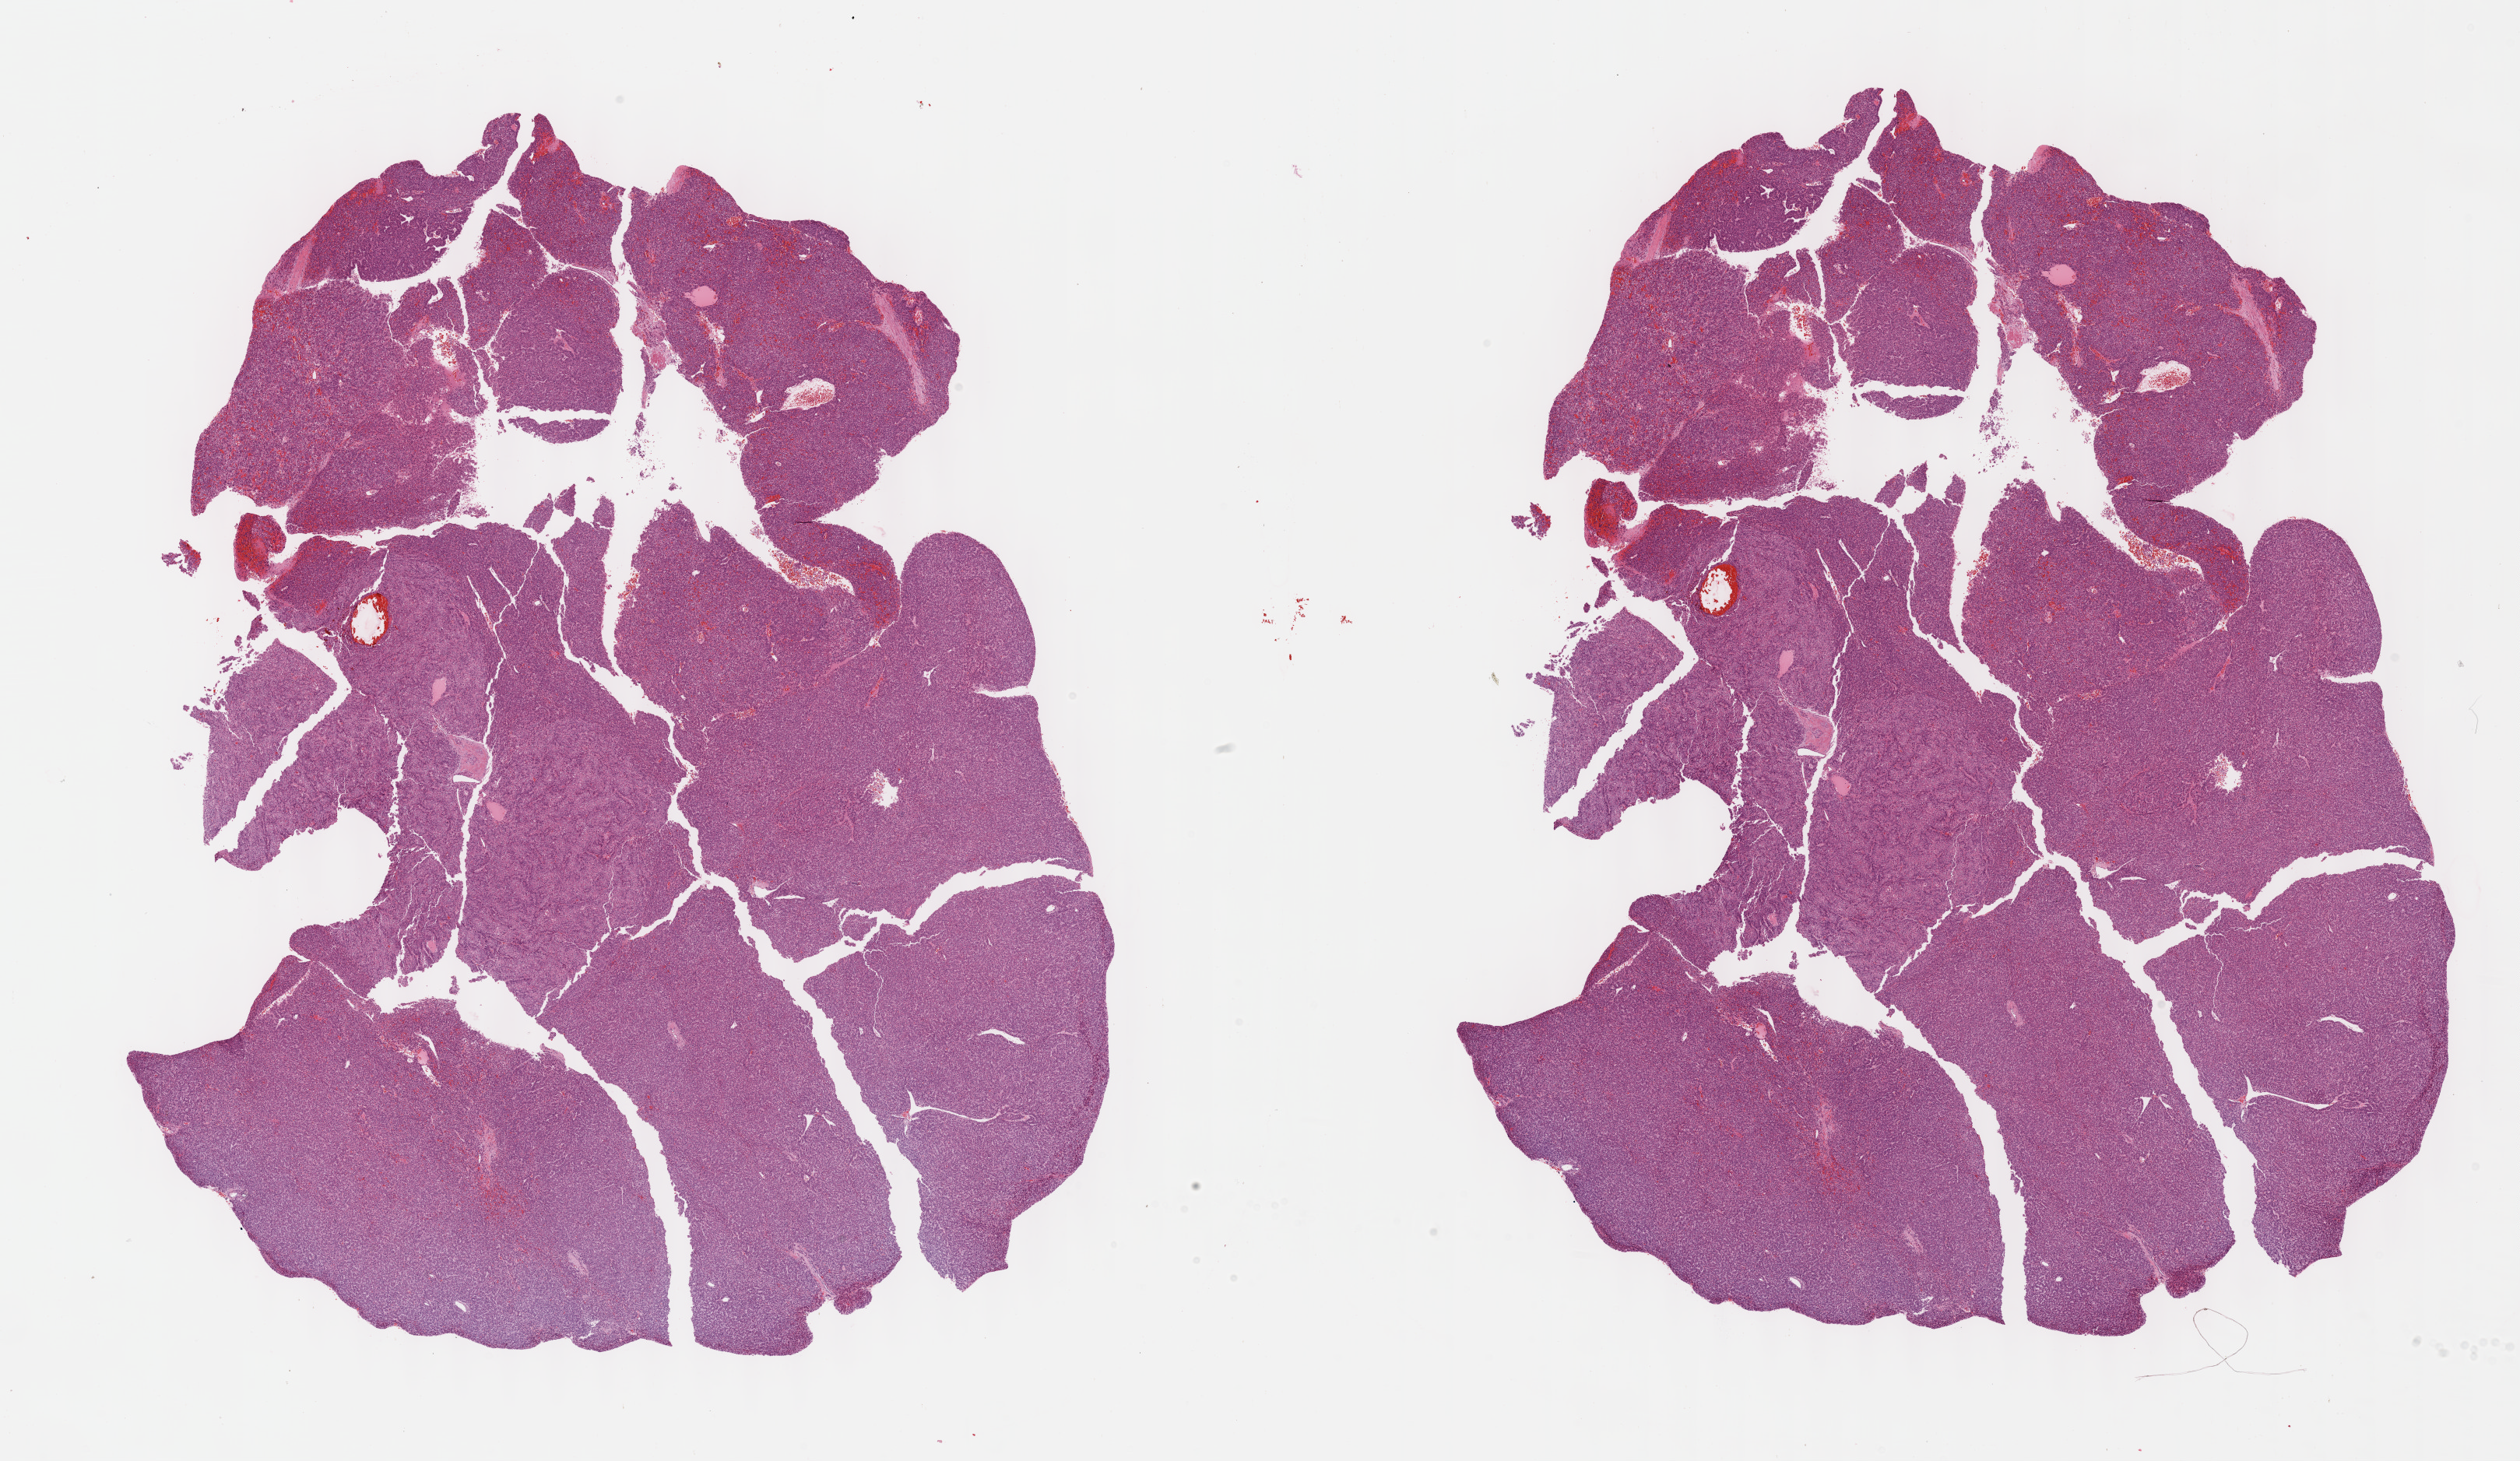
Whole-slide histology image, H&E, low-resolution overview of the scanned area, about 26.2 x 15.2 mm (slide scanned at 40x); formalin-fixed paraffin-embedded (FFPE) diagnostic section; primary tumour sample from the liver. Male patient; age at initial diagnosis 43 years. Histologic grade: G3 (poorly differentiated).
* AJCC pathologic stage: I (7th edition)
* histologic diagnosis: Hepatocellular carcinoma, NOS
* TNM: T1 N0 M0